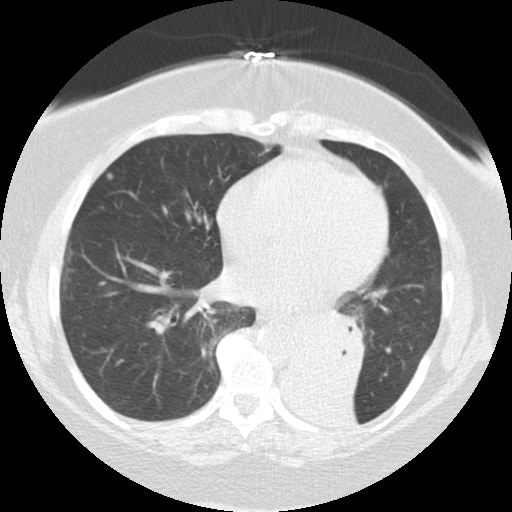
Low-dose screening chest CT, axial slice; baseline screening round; lung window (W 1500 / L -600 HU); standard (soft-tissue) reconstruction kernel (STANDARD). Female participant, aged 71 years at enrolment.
Lesion marked by an expert reader, bounding box <281,303,369,384> (left, top, right, bottom; pixels). Screening reader's record for this exam (one nodule recorded; not confirmed to be the boxed lesion): non-calcified nodule or mass ≥4 mm, right middle lobe, 5 × 5 mm, smooth margins, soft tissue attenuation. Note: the box lies in the patient's left hemithorax on this image, whereas the reader's record names the right lung; they may be different findings. Official screen result: positive, change unspecified: nodule(s) >= 4 mm or enlarging nodule(s), mass(es), or other non-specific abnormalities suspicious for lung cancer.